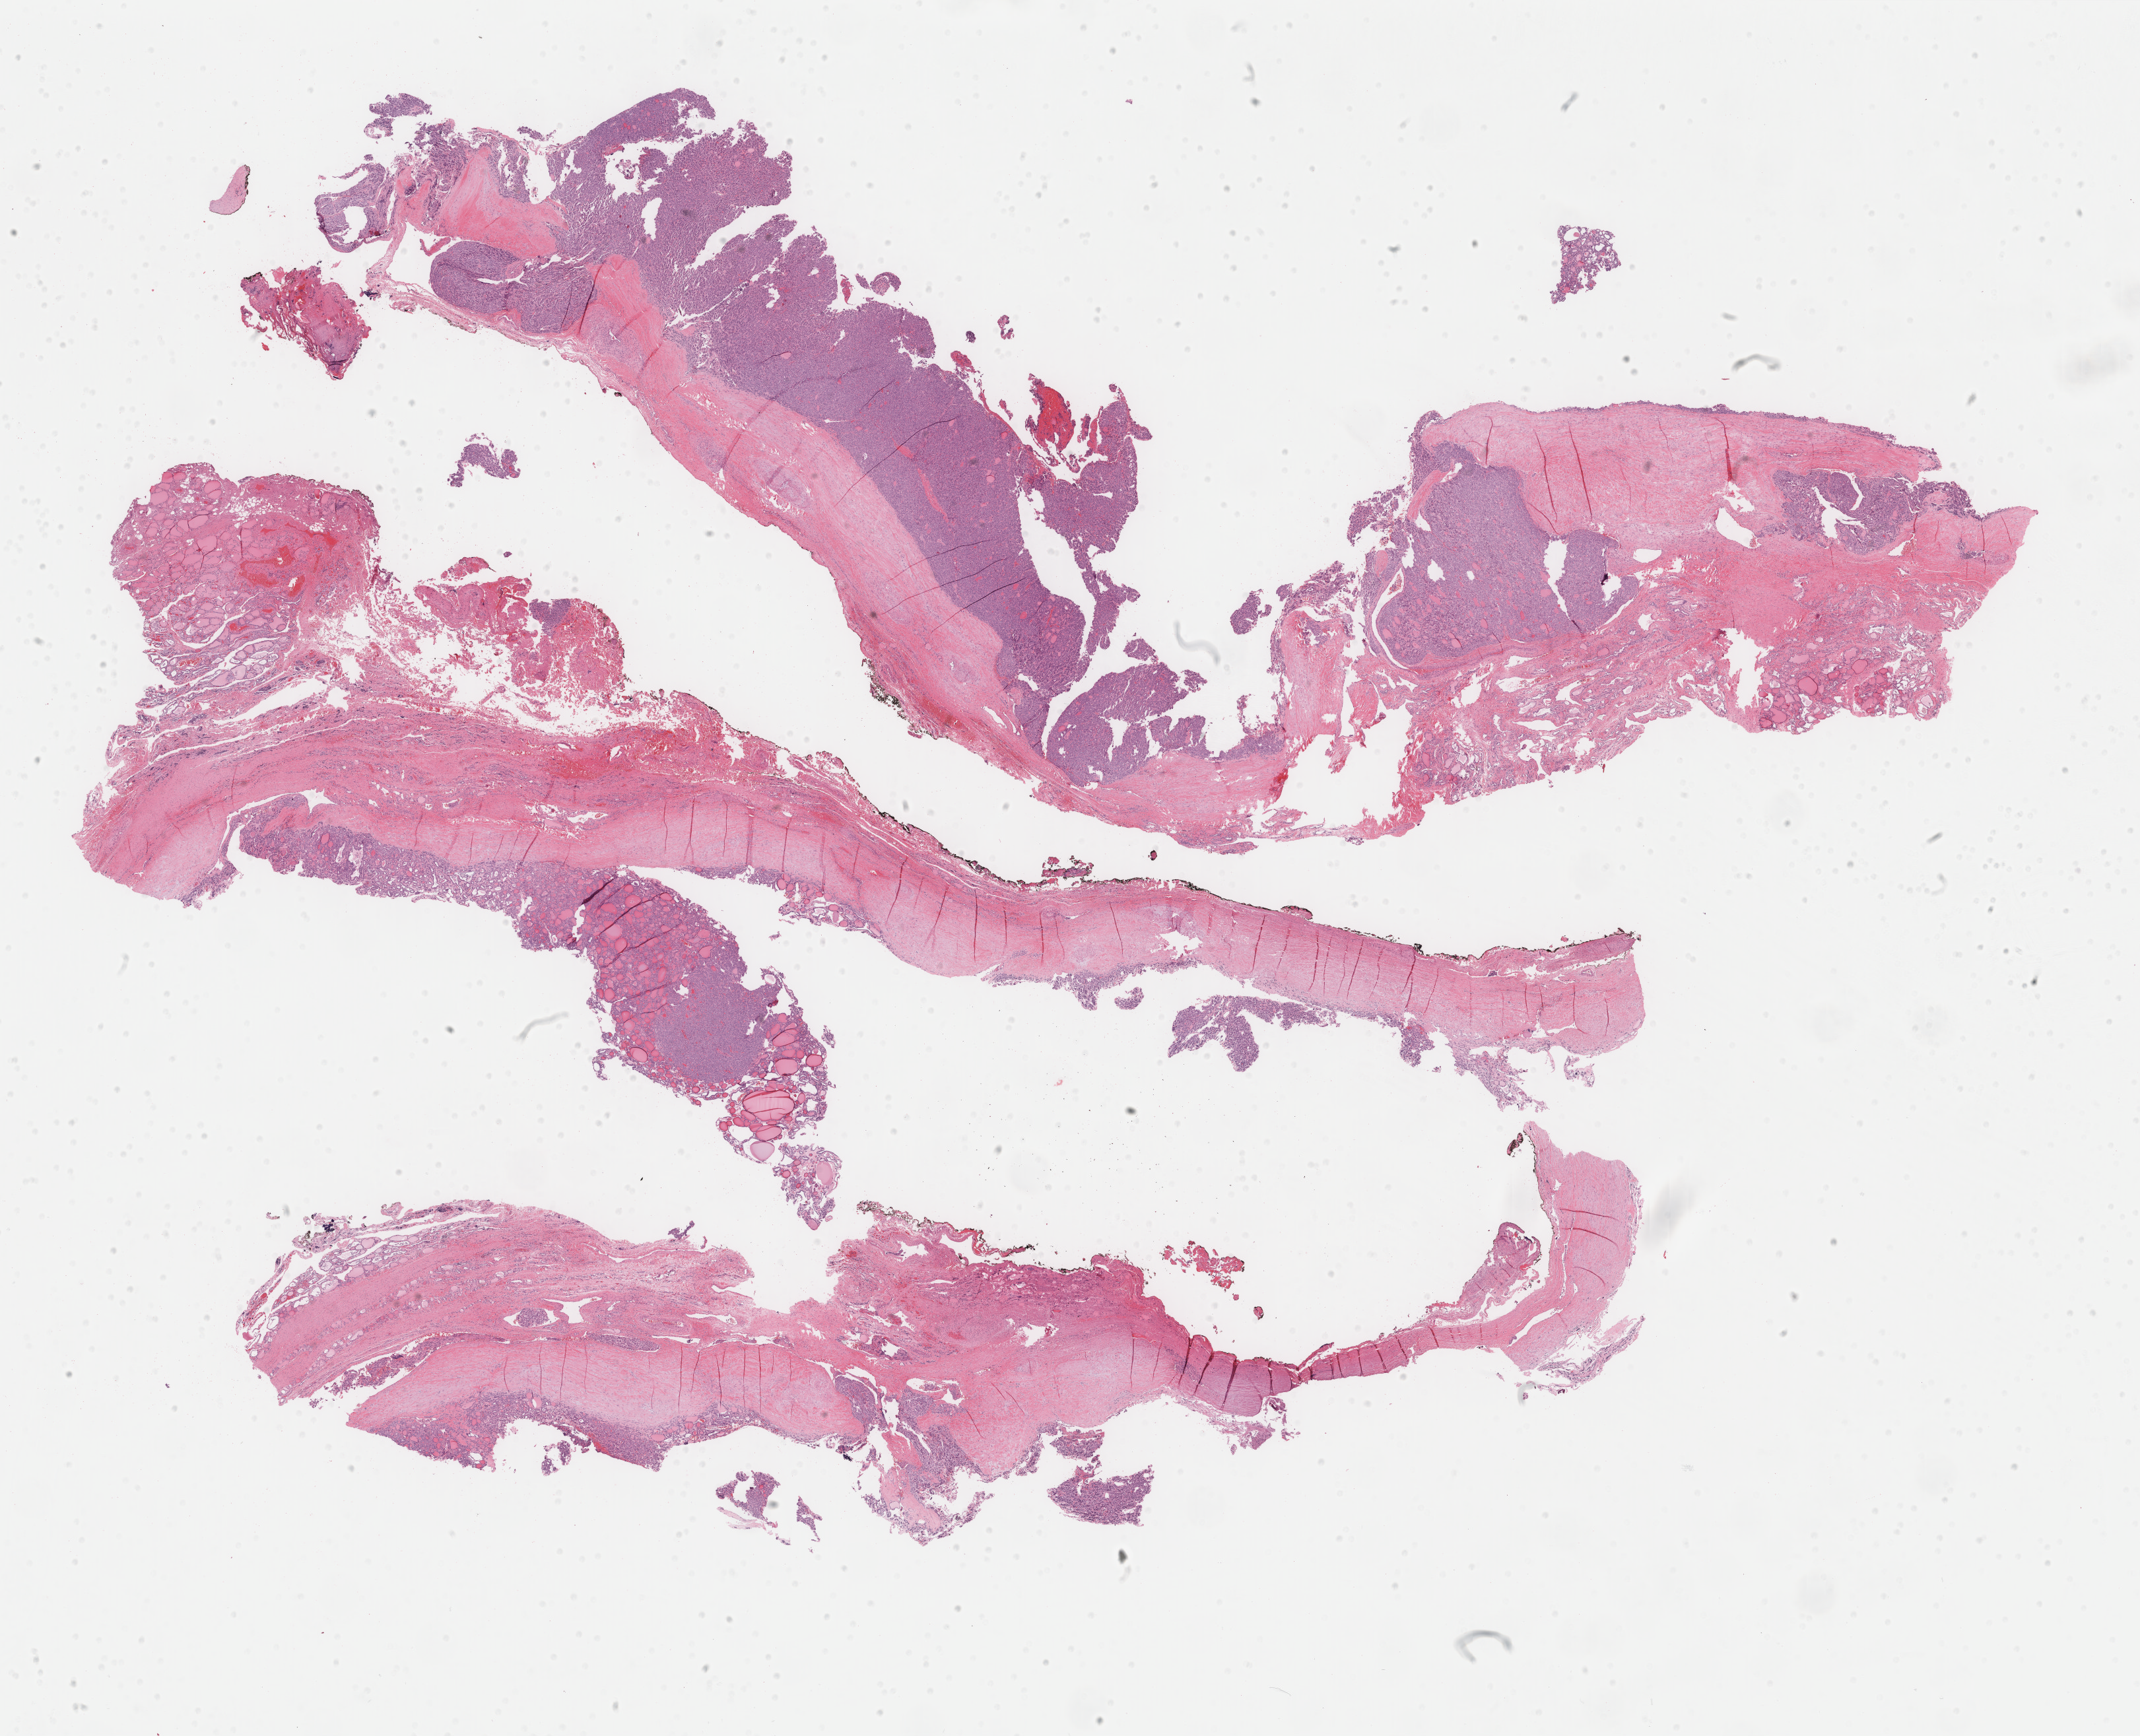
Digitized H&E-stained tissue section (whole slide), low-resolution overview of the scanned area, about 25.7 x 20.9 mm. Formalin-fixed paraffin-embedded (FFPE) diagnostic section. Primary tumour sample from the thyroid. Female, age 30 years at initial diagnosis.
- AJCC pathologic stage: I
- pathologic diagnosis: Papillary adenocarcinoma, NOS